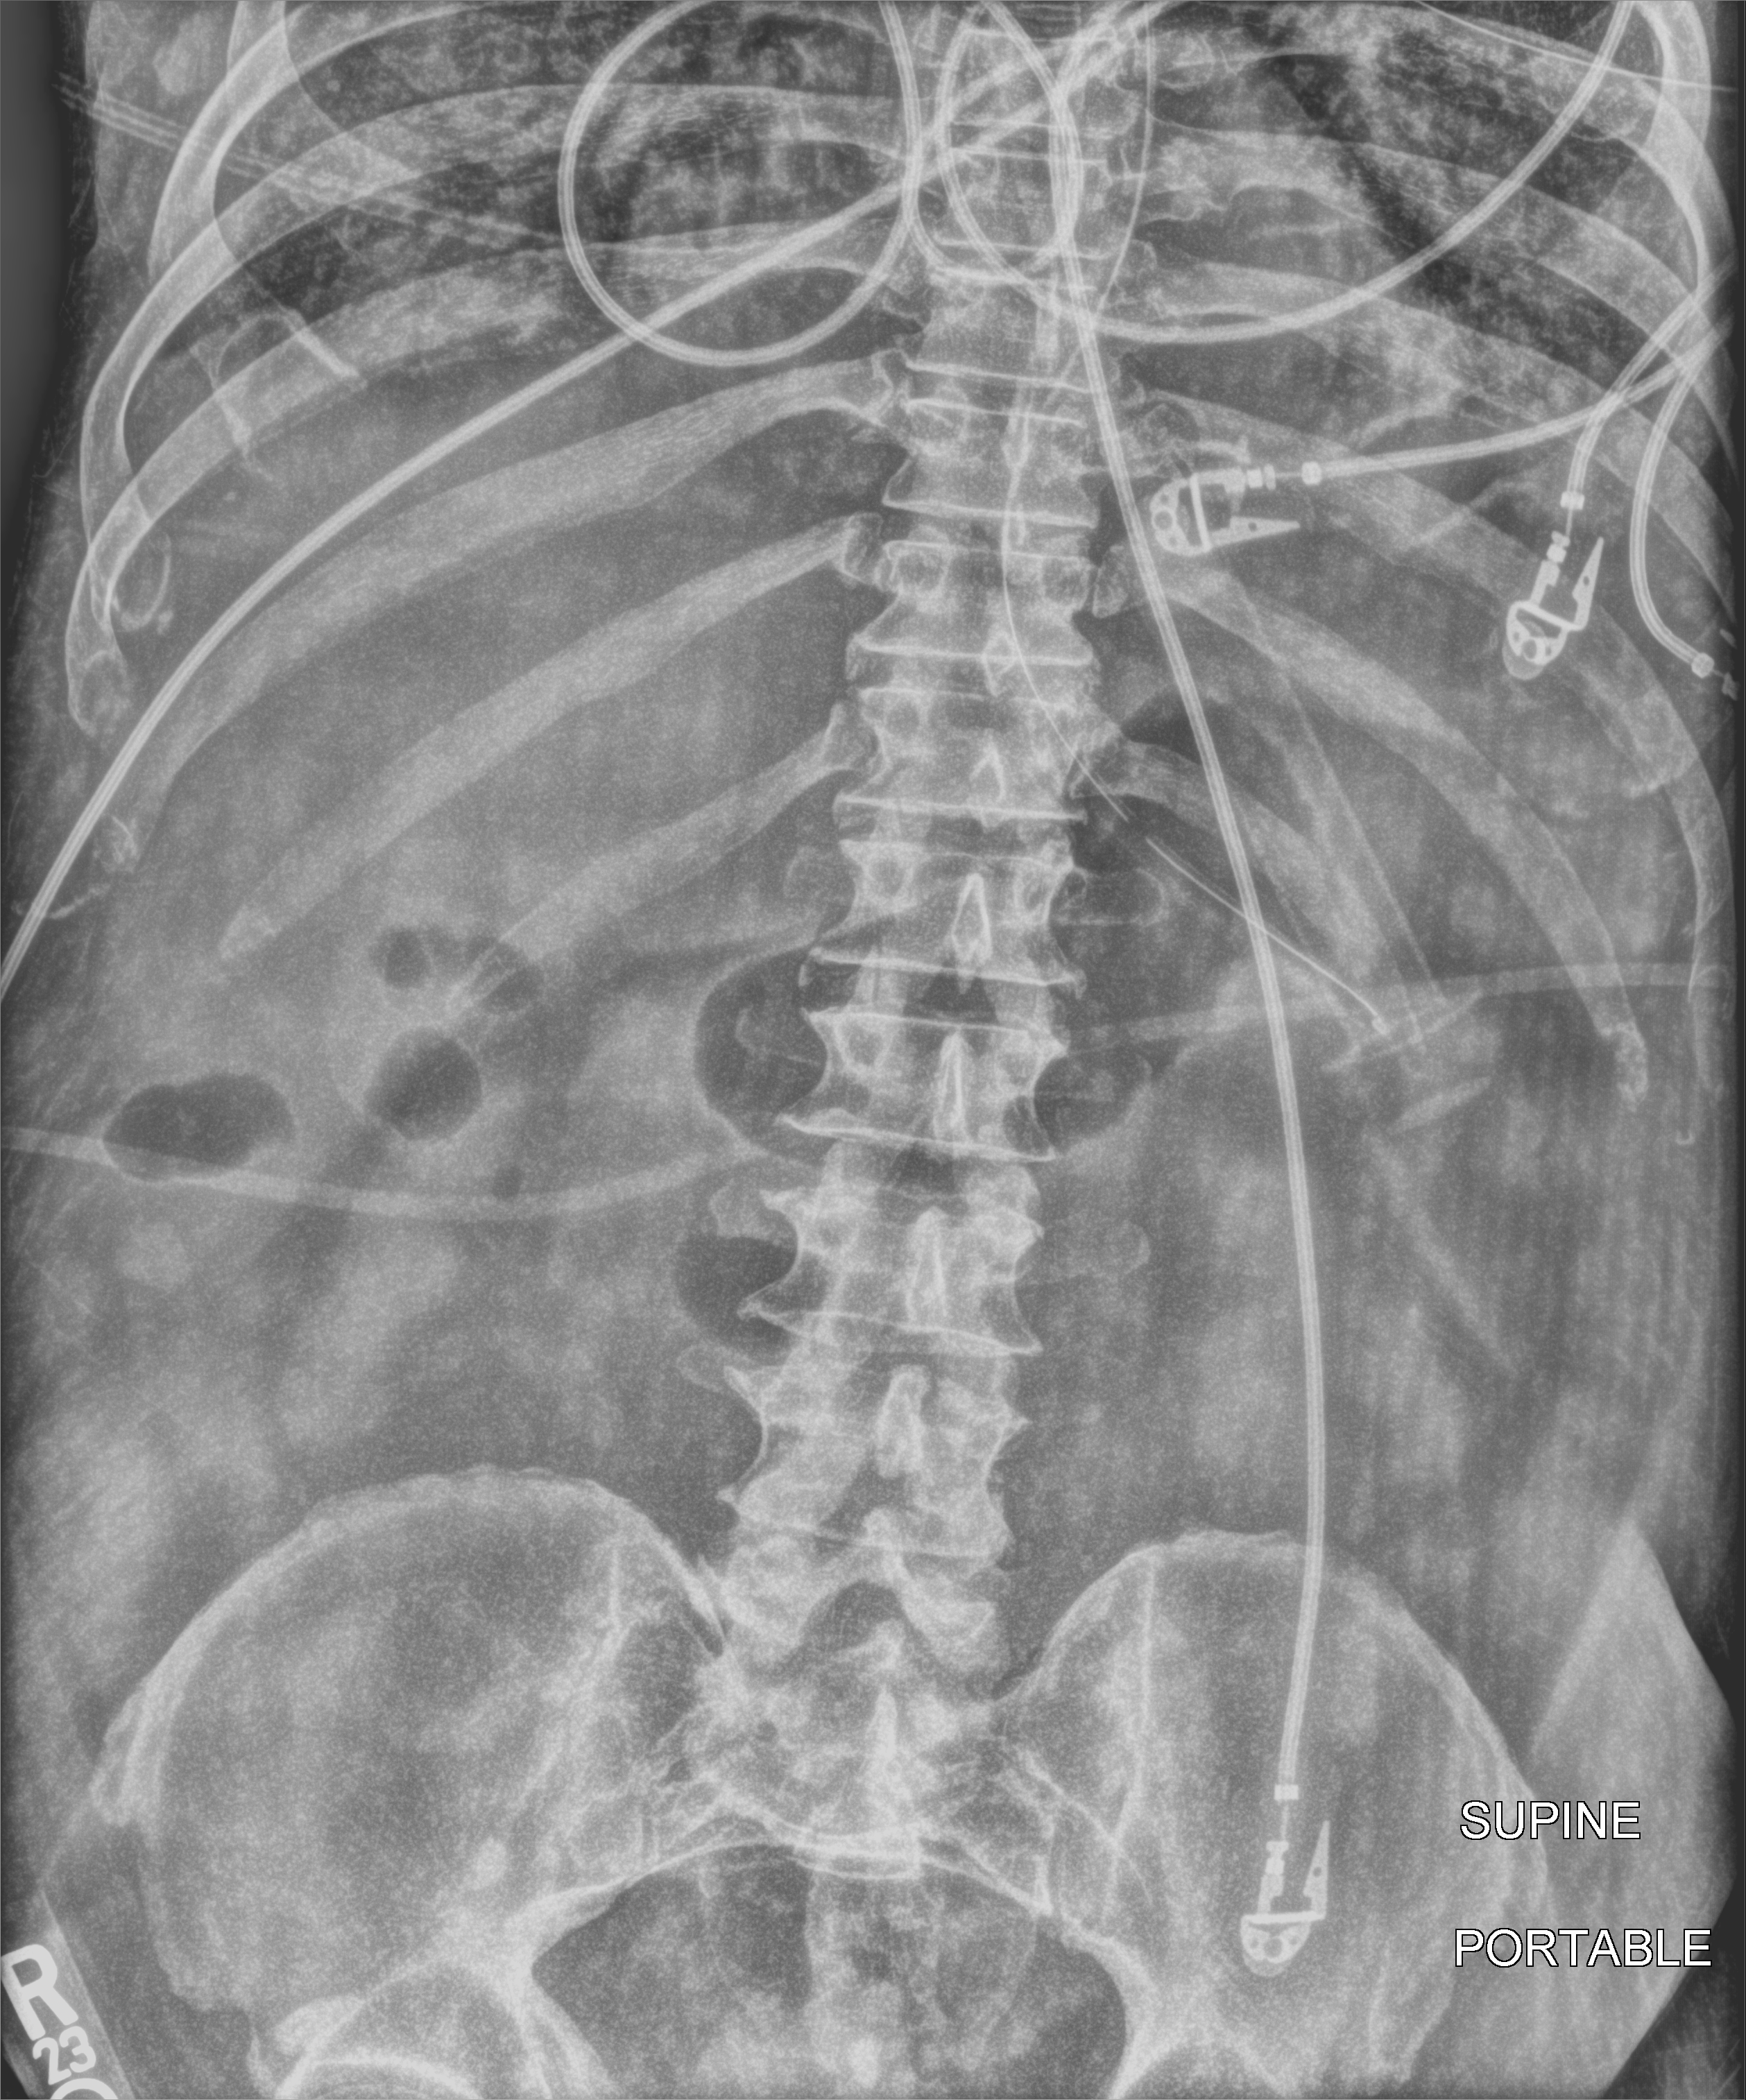
Portable abdomen radiograph, anteroposterior (AP) projection. Patient hospitalised with COVID-19; male, aged 60–74 years.
Hospital-stay facts (about this admission, not read from this image; timing relative to this image not recorded):
- length of hospital stay: 28 days